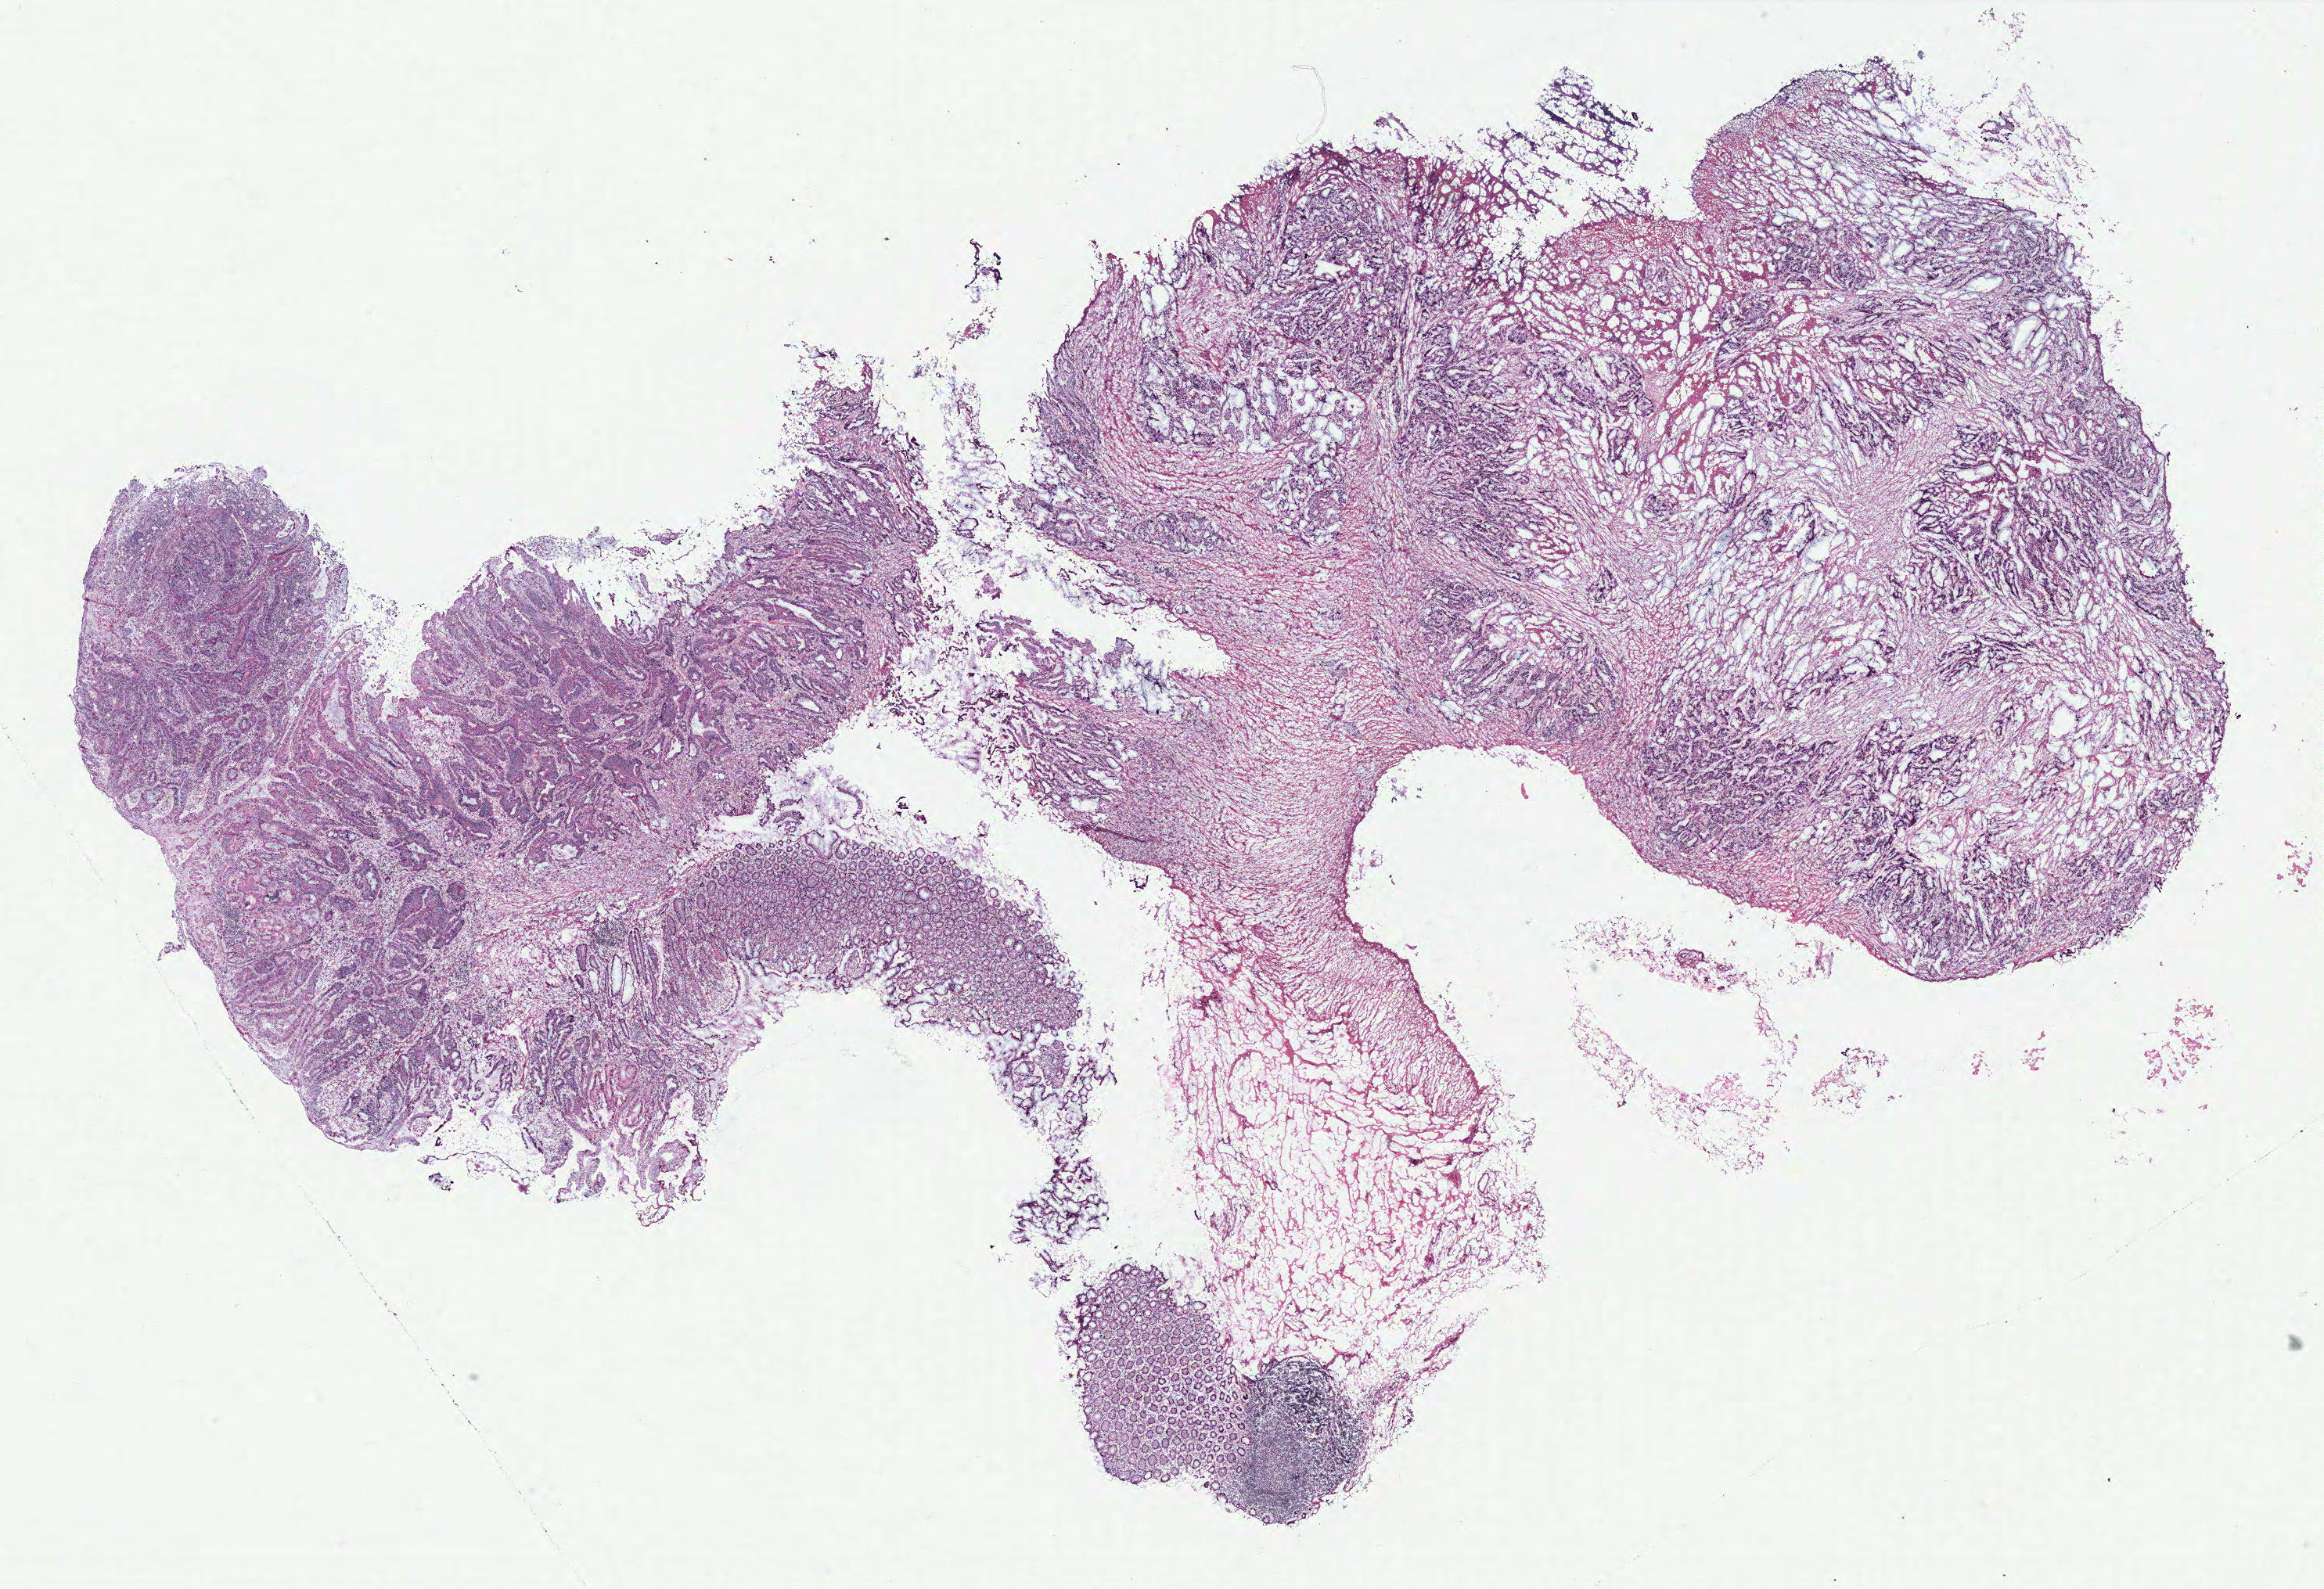
H&E-stained whole-slide image — low-resolution overview of the scanned area, about 23.8 x 16.3 mm (acquisition: 40x scan). Colon, tissue type not recorded.
Patient diagnosis (cohort enrolment): colon cancer (colon).